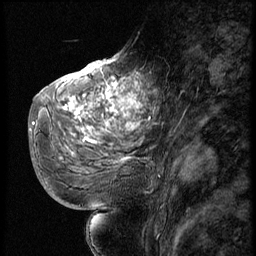
Breast MRI (dynamic contrast-enhanced), one sagittal slice; position 30 of 56 along the scan axis; 3 images stored at this slice position (order not interpretable as contrast timing); 1.5 T; TE 4.2 ms, TR 9 ms; 2.5 mm slice thickness; 256 × 256 image matrix, field of view 180 × 180 mm. Female patient, age 51 years. Case-level facts recorded for this patient, not image findings: setting: breast cancer imaged before/during neoadjuvant chemotherapy; receptor status: triple-negative.
Outlined on this slice (semi-automatically segmented with operator editing):
- analysis volume of interest (the breast-tissue region the enhancement analysis was run in; not a lesion): bounding box (x1, y1, x2, y2) in pixels: (52, 66, 145, 179)
- tumour enhancement mask (voxels above the 140 % enhancement threshold inside the analysis volume of interest): (63, 68, 144, 161)